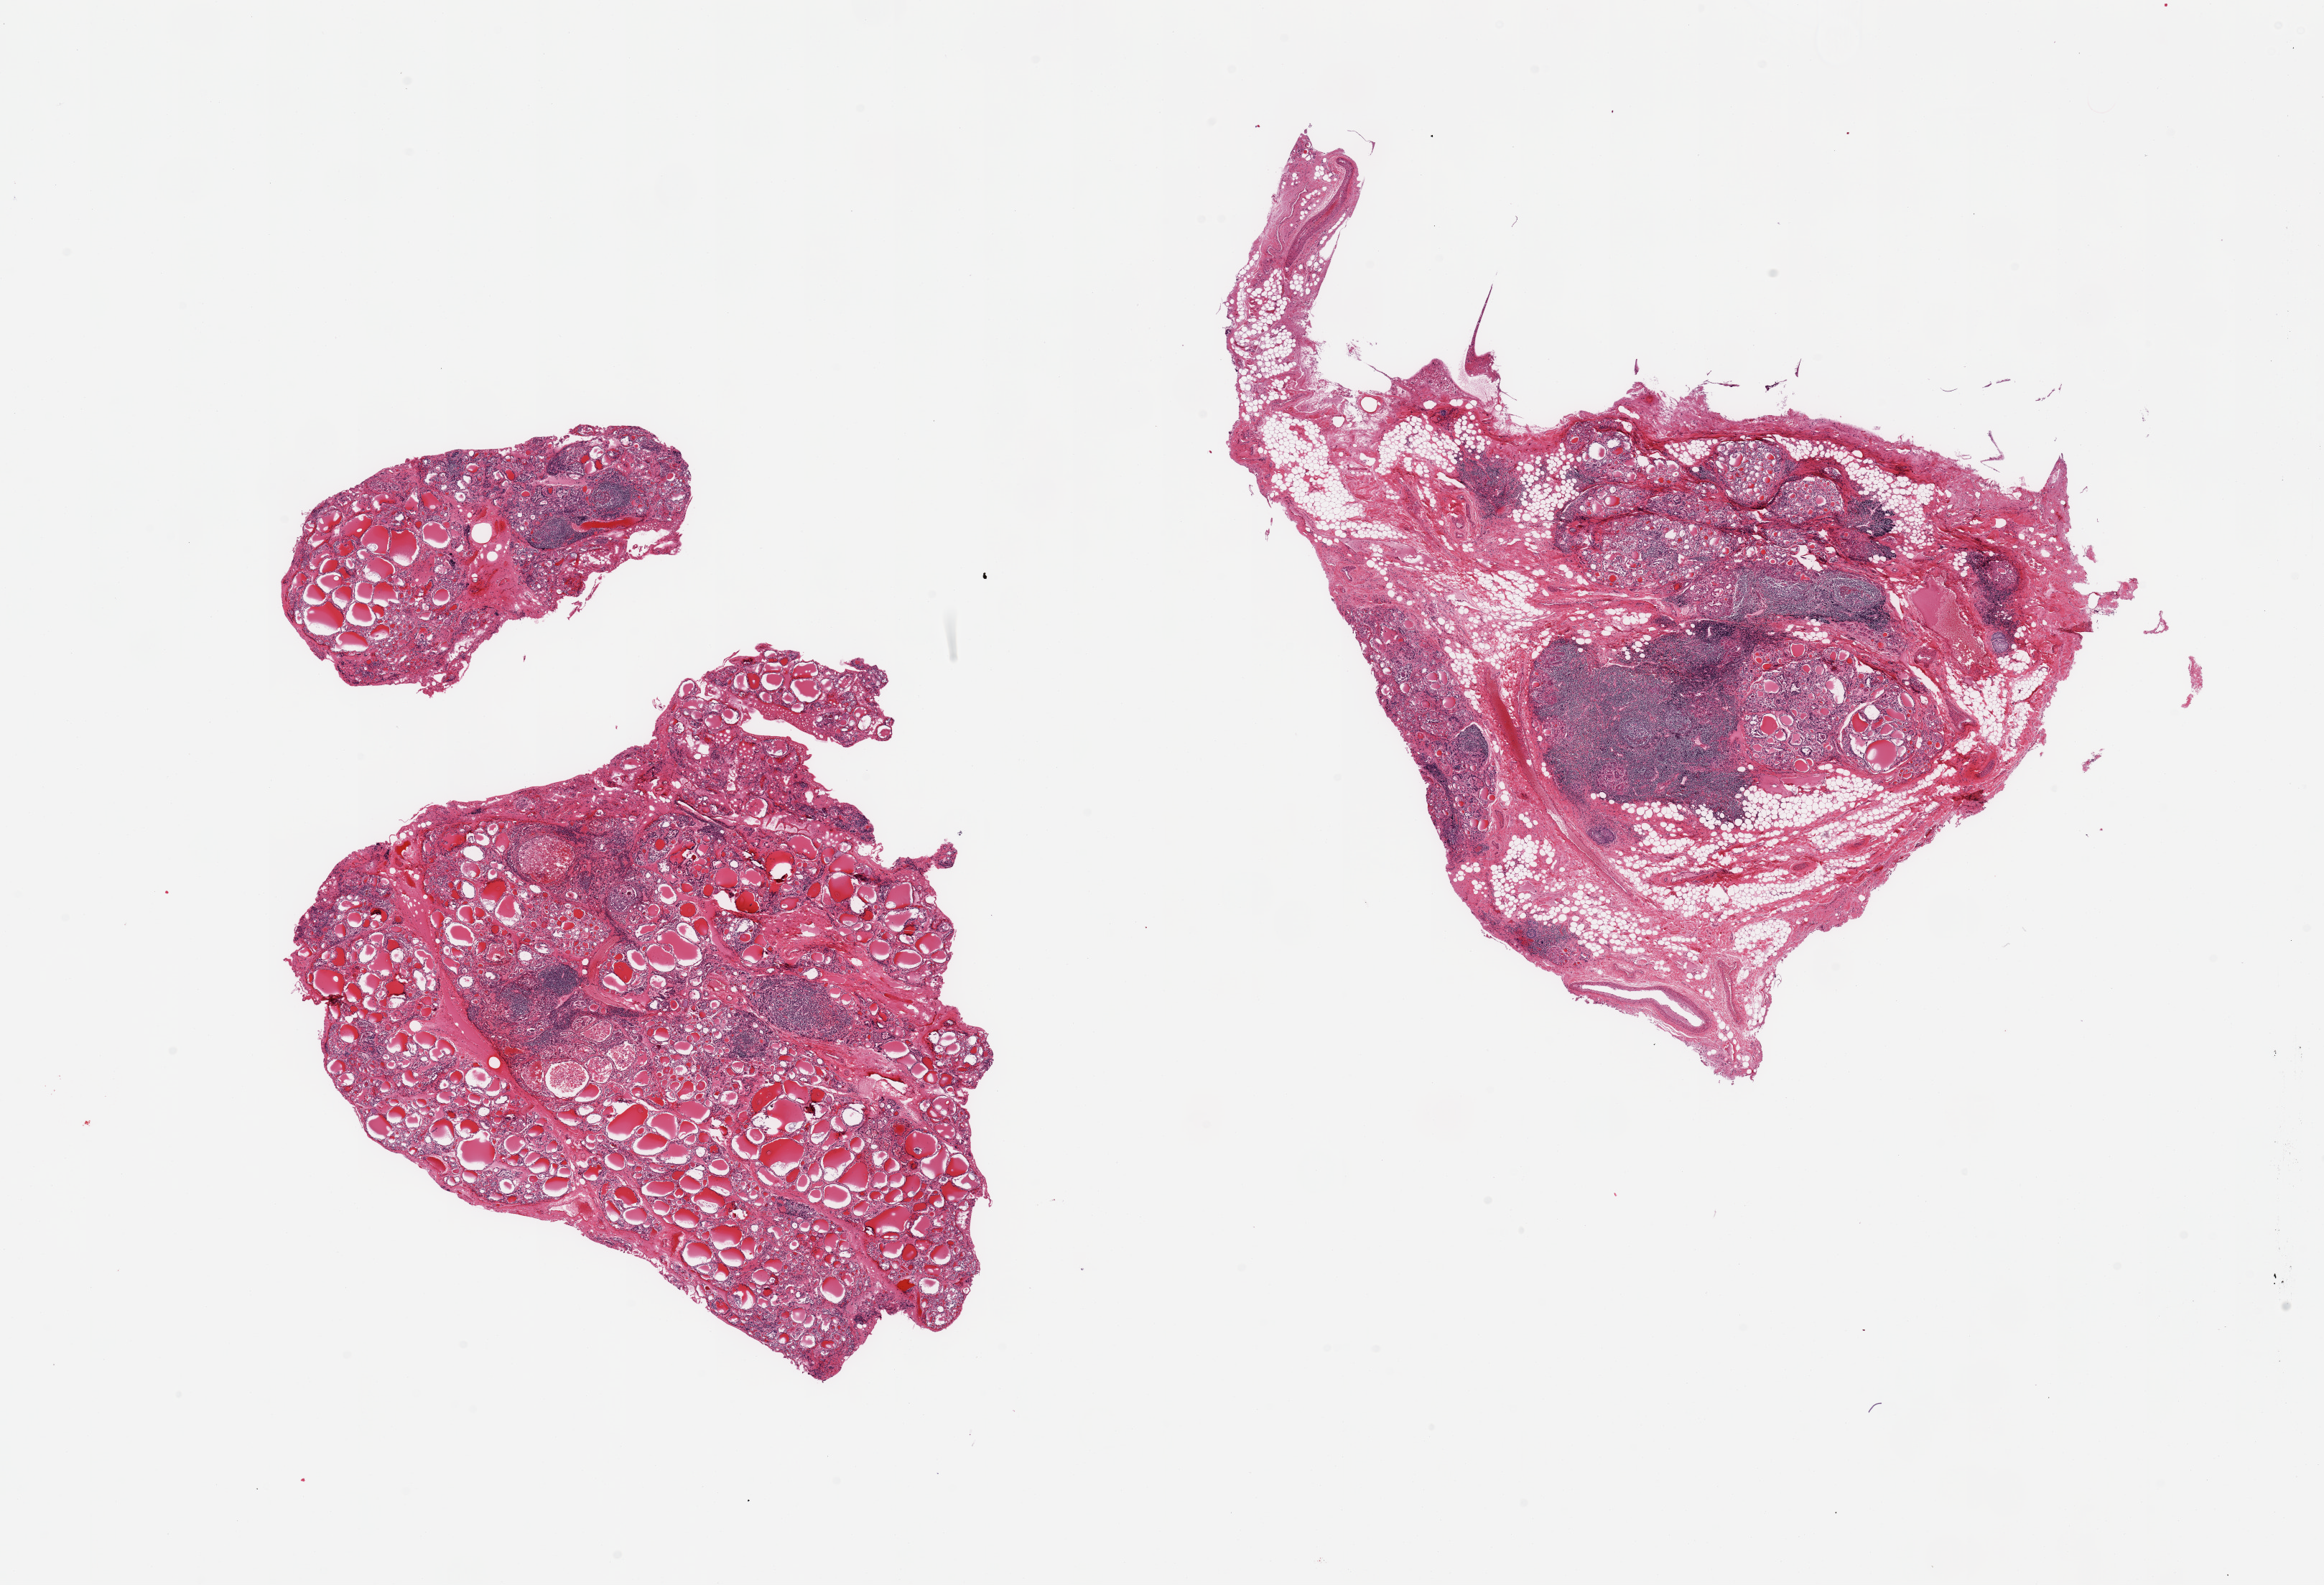
Whole-slide image, hematoxylin and eosin (H&E) stain, brightfield — whole scanned area (about 25.6 x 17.5 mm) shown as a low-resolution overview; PAXgene-fixed paraffin-embedded (PFPE) section; target tissue: thyroid; tissue donor sample. Donor sex: female.
* reviewer comment on this tissue sample: 2 pieces; nodular goiter, Hashimoto thyroiditis, one piece includes ~50% fat/fibrovascular tissue